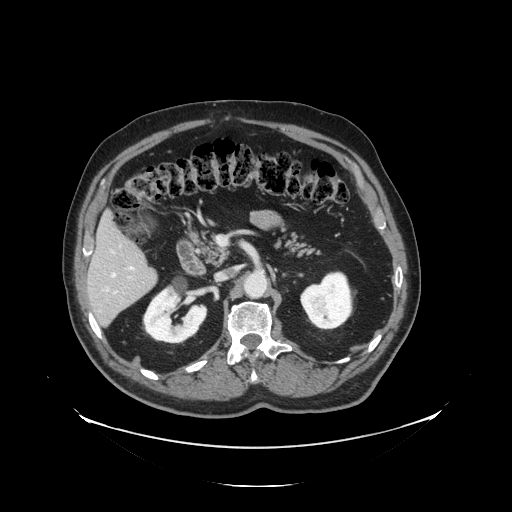
Contrast-enhanced abdominal CT, one axial slice. 120 kVp. Intravenous contrast given. Soft-tissue window (W 400 / L 40 HU). 2.5 mm slice thickness. 512 × 512 image matrix, field of view 497 × 497 mm. Male patient, age 77 years. From the clinical record (not read from this slice): diagnosis: colorectal cancer liver metastases, imaged before liver resection; multiple liver metastases: no.
Annotated regions visible in this slice (outlined manually by an expert reader):
- liver: bounding box [x1, y1, x2, y2] px = [89, 216, 157, 327]
- planned liver remnant (the part of the liver to remain after resection): [89, 216, 149, 286]
- portal vein (with intrahepatic branches): [115, 268, 133, 293]